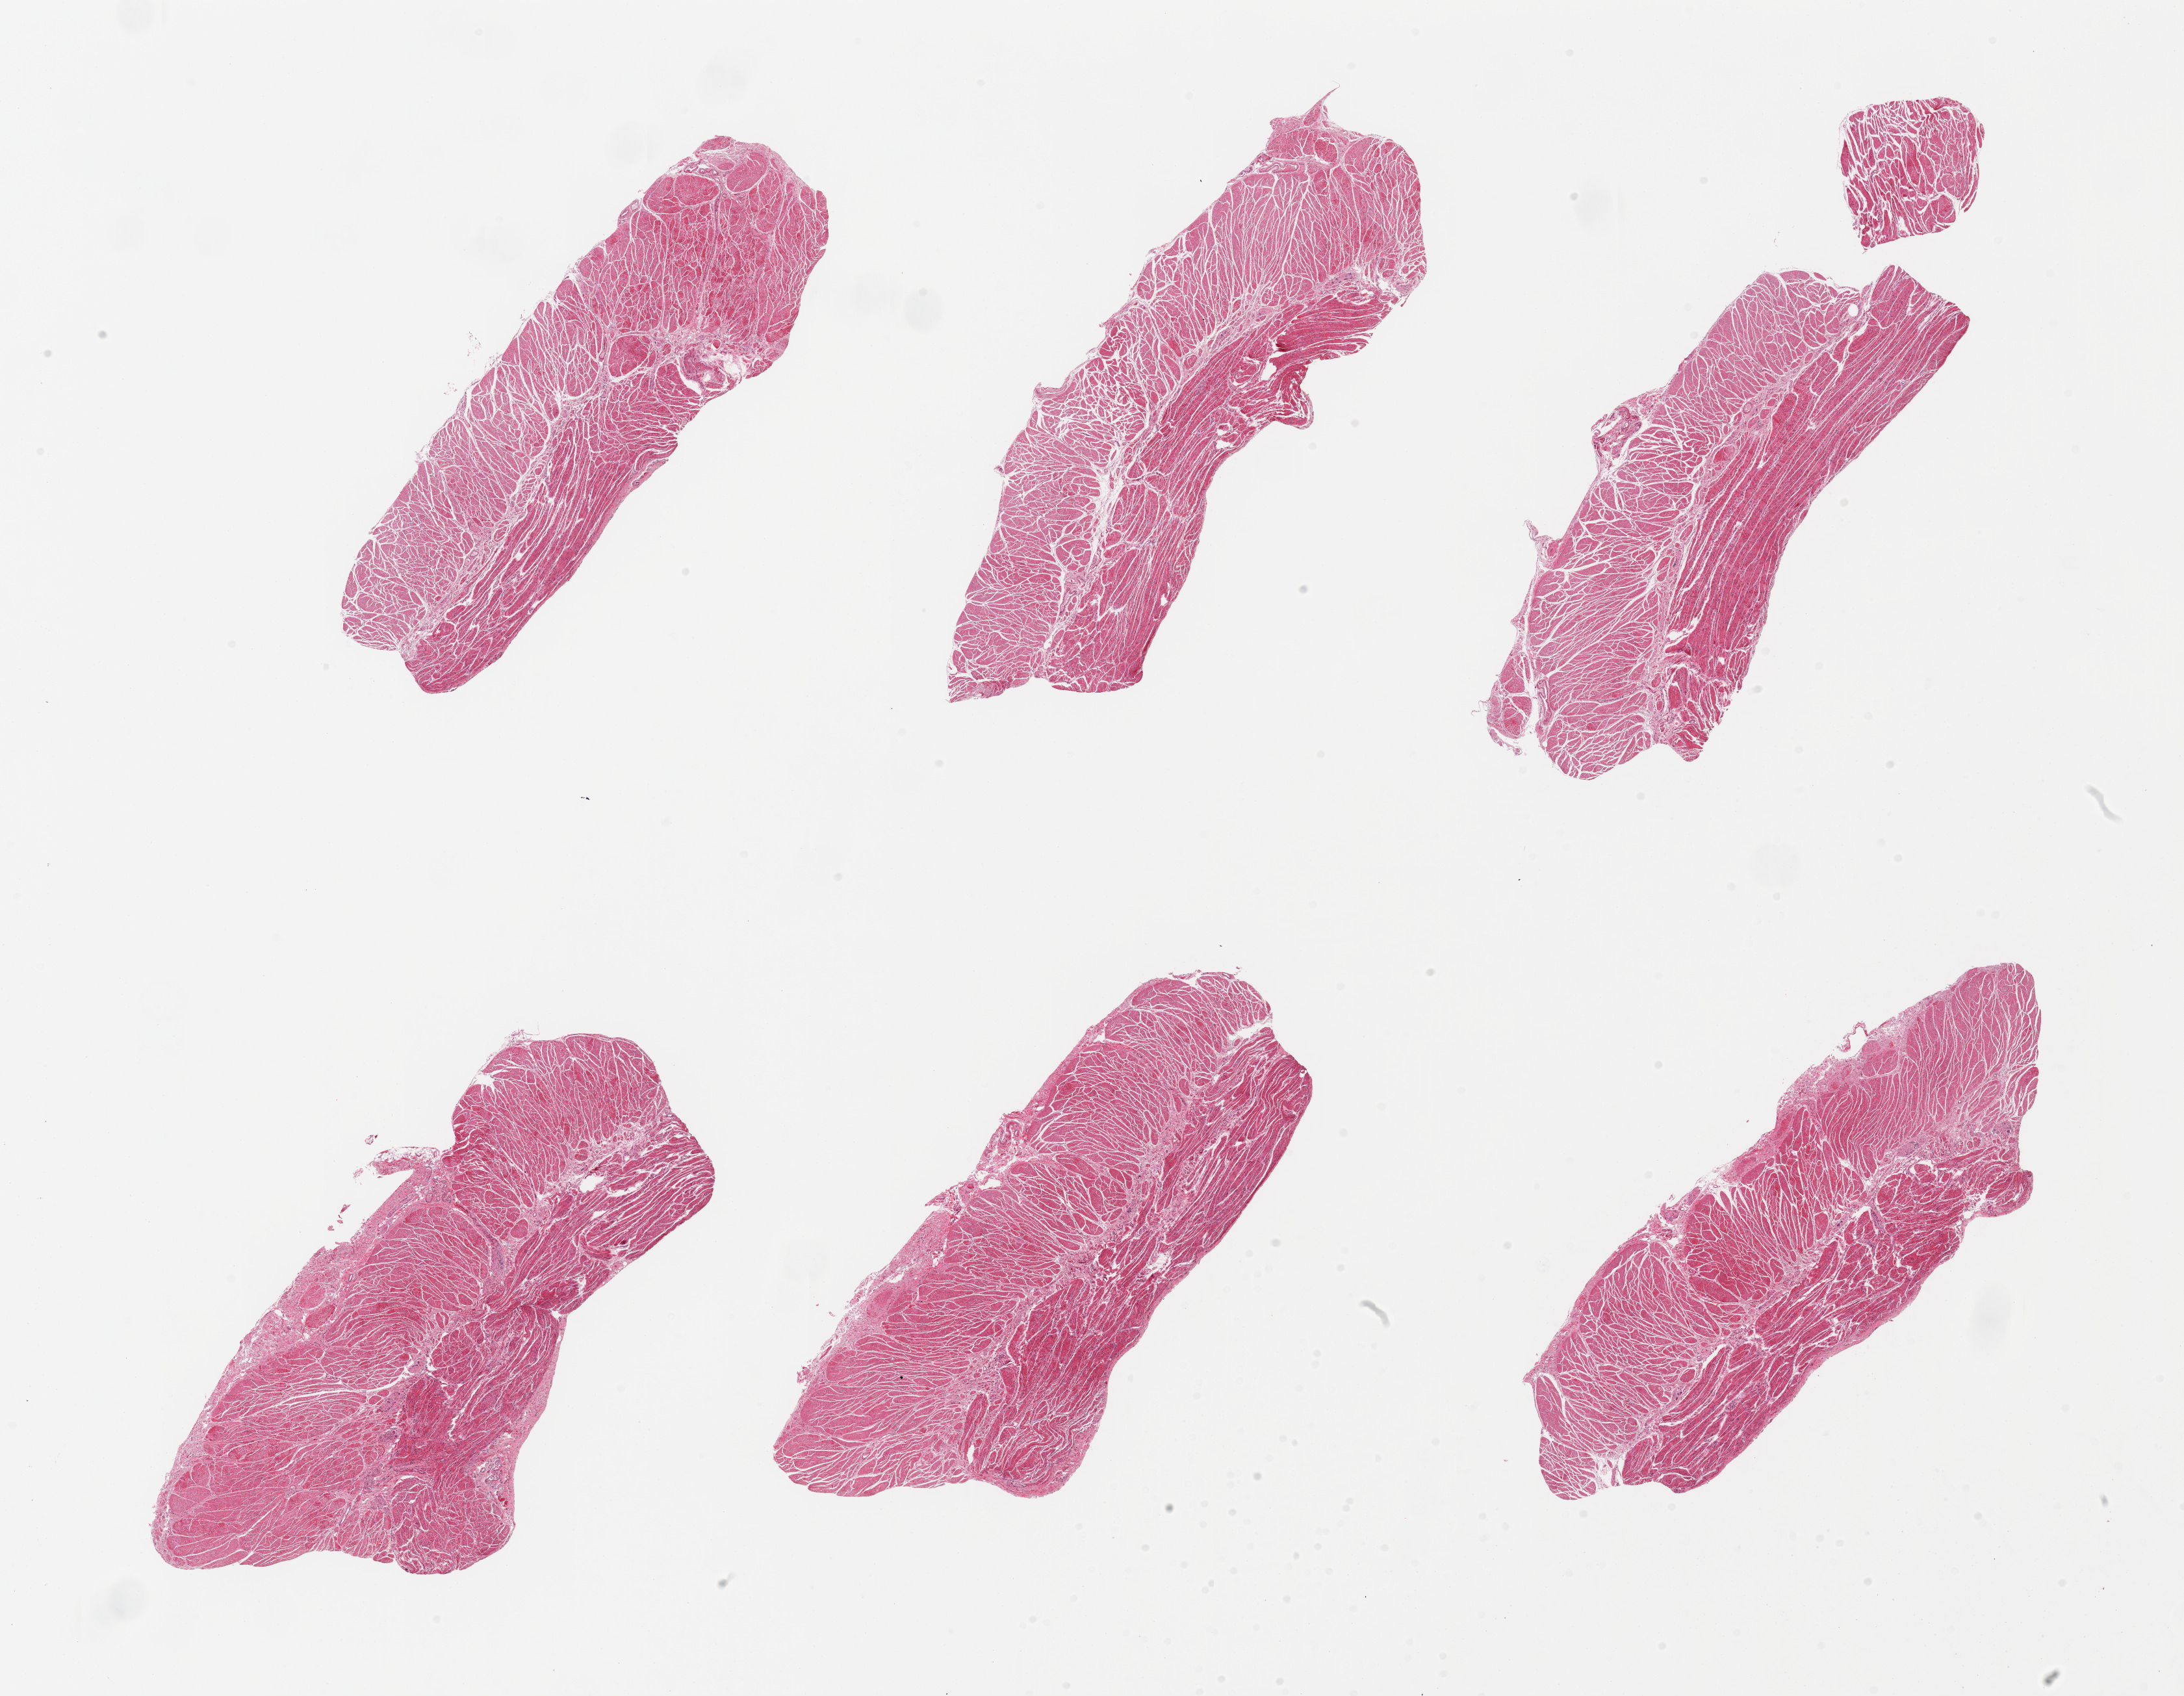
Whole-slide image, H&E stain — whole scanned area (about 26.6 x 20.6 mm, from a 20x scan) shown as a low-resolution overview, PAXgene-fixed, paraffin-embedded tissue, target tissue: gastroesophageal junction, donor tissue sample.
Reviewer comment on this tissue sample: 6 pieces, confirmed target muscularis.